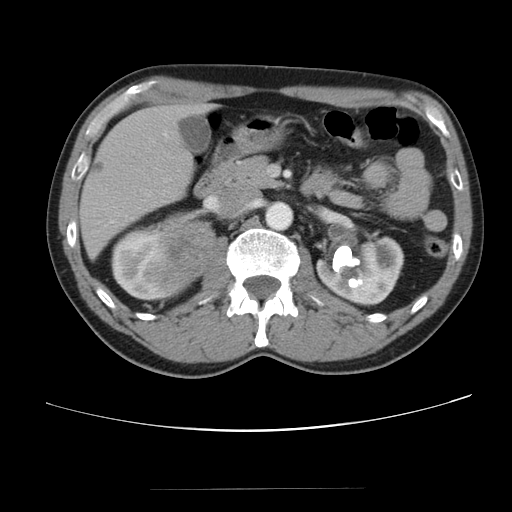
Contrast-enhanced abdominal CT, one axial slice; slice 58 of 80 in the series (ordered by position); reconstruction kernel STANDARD; 120 kVp; intravenous contrast given; soft-tissue window (W 400 / L 40 HU); 5 mm slice thickness; 512 × 512 image matrix, field of view 360 × 360 mm. Patient: male, 61 years. Case-level facts recorded for this patient, not image findings: diagnosis: adrenocortical carcinoma; tumour side: right adrenal; tumour size at pathology: 11.1 cm; Ki-67 index: 32 %; stage (as recorded): 2.
Structures marked on this image (semi-automatic segmentation, software-assisted and operator-edited):
- mass: bounding box <164,218,214,282> (left, top, right, bottom; pixels)